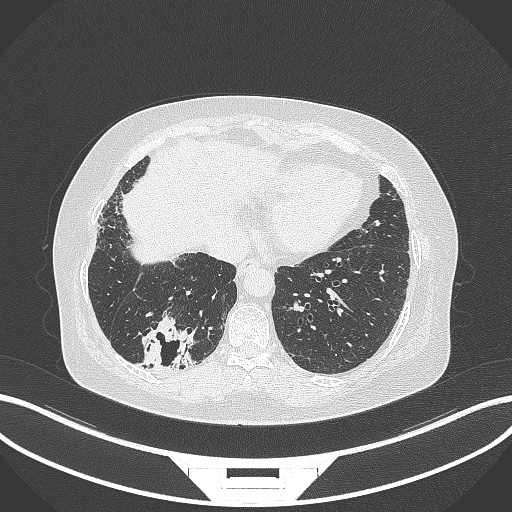
Chest CT, one axial slice. Position 53 of 296 along the scan axis. Reconstruction kernel B70f. 120 kVp. Lung window (W 1500 / L -600 HU). 512 × 512 image matrix, field of view 400 × 400 mm. Patient: female, 65 years. Case-level facts recorded for this patient, not image findings: clinical TNM (as recorded): T2b N1 M0; histopathological grade: G1.
Annotated regions visible in this slice (rectangle marked by the reading radiologist):
- lung tumour (recorded histology: adenocarcinoma): box from (x=137, y=313) to (x=195, y=371) px